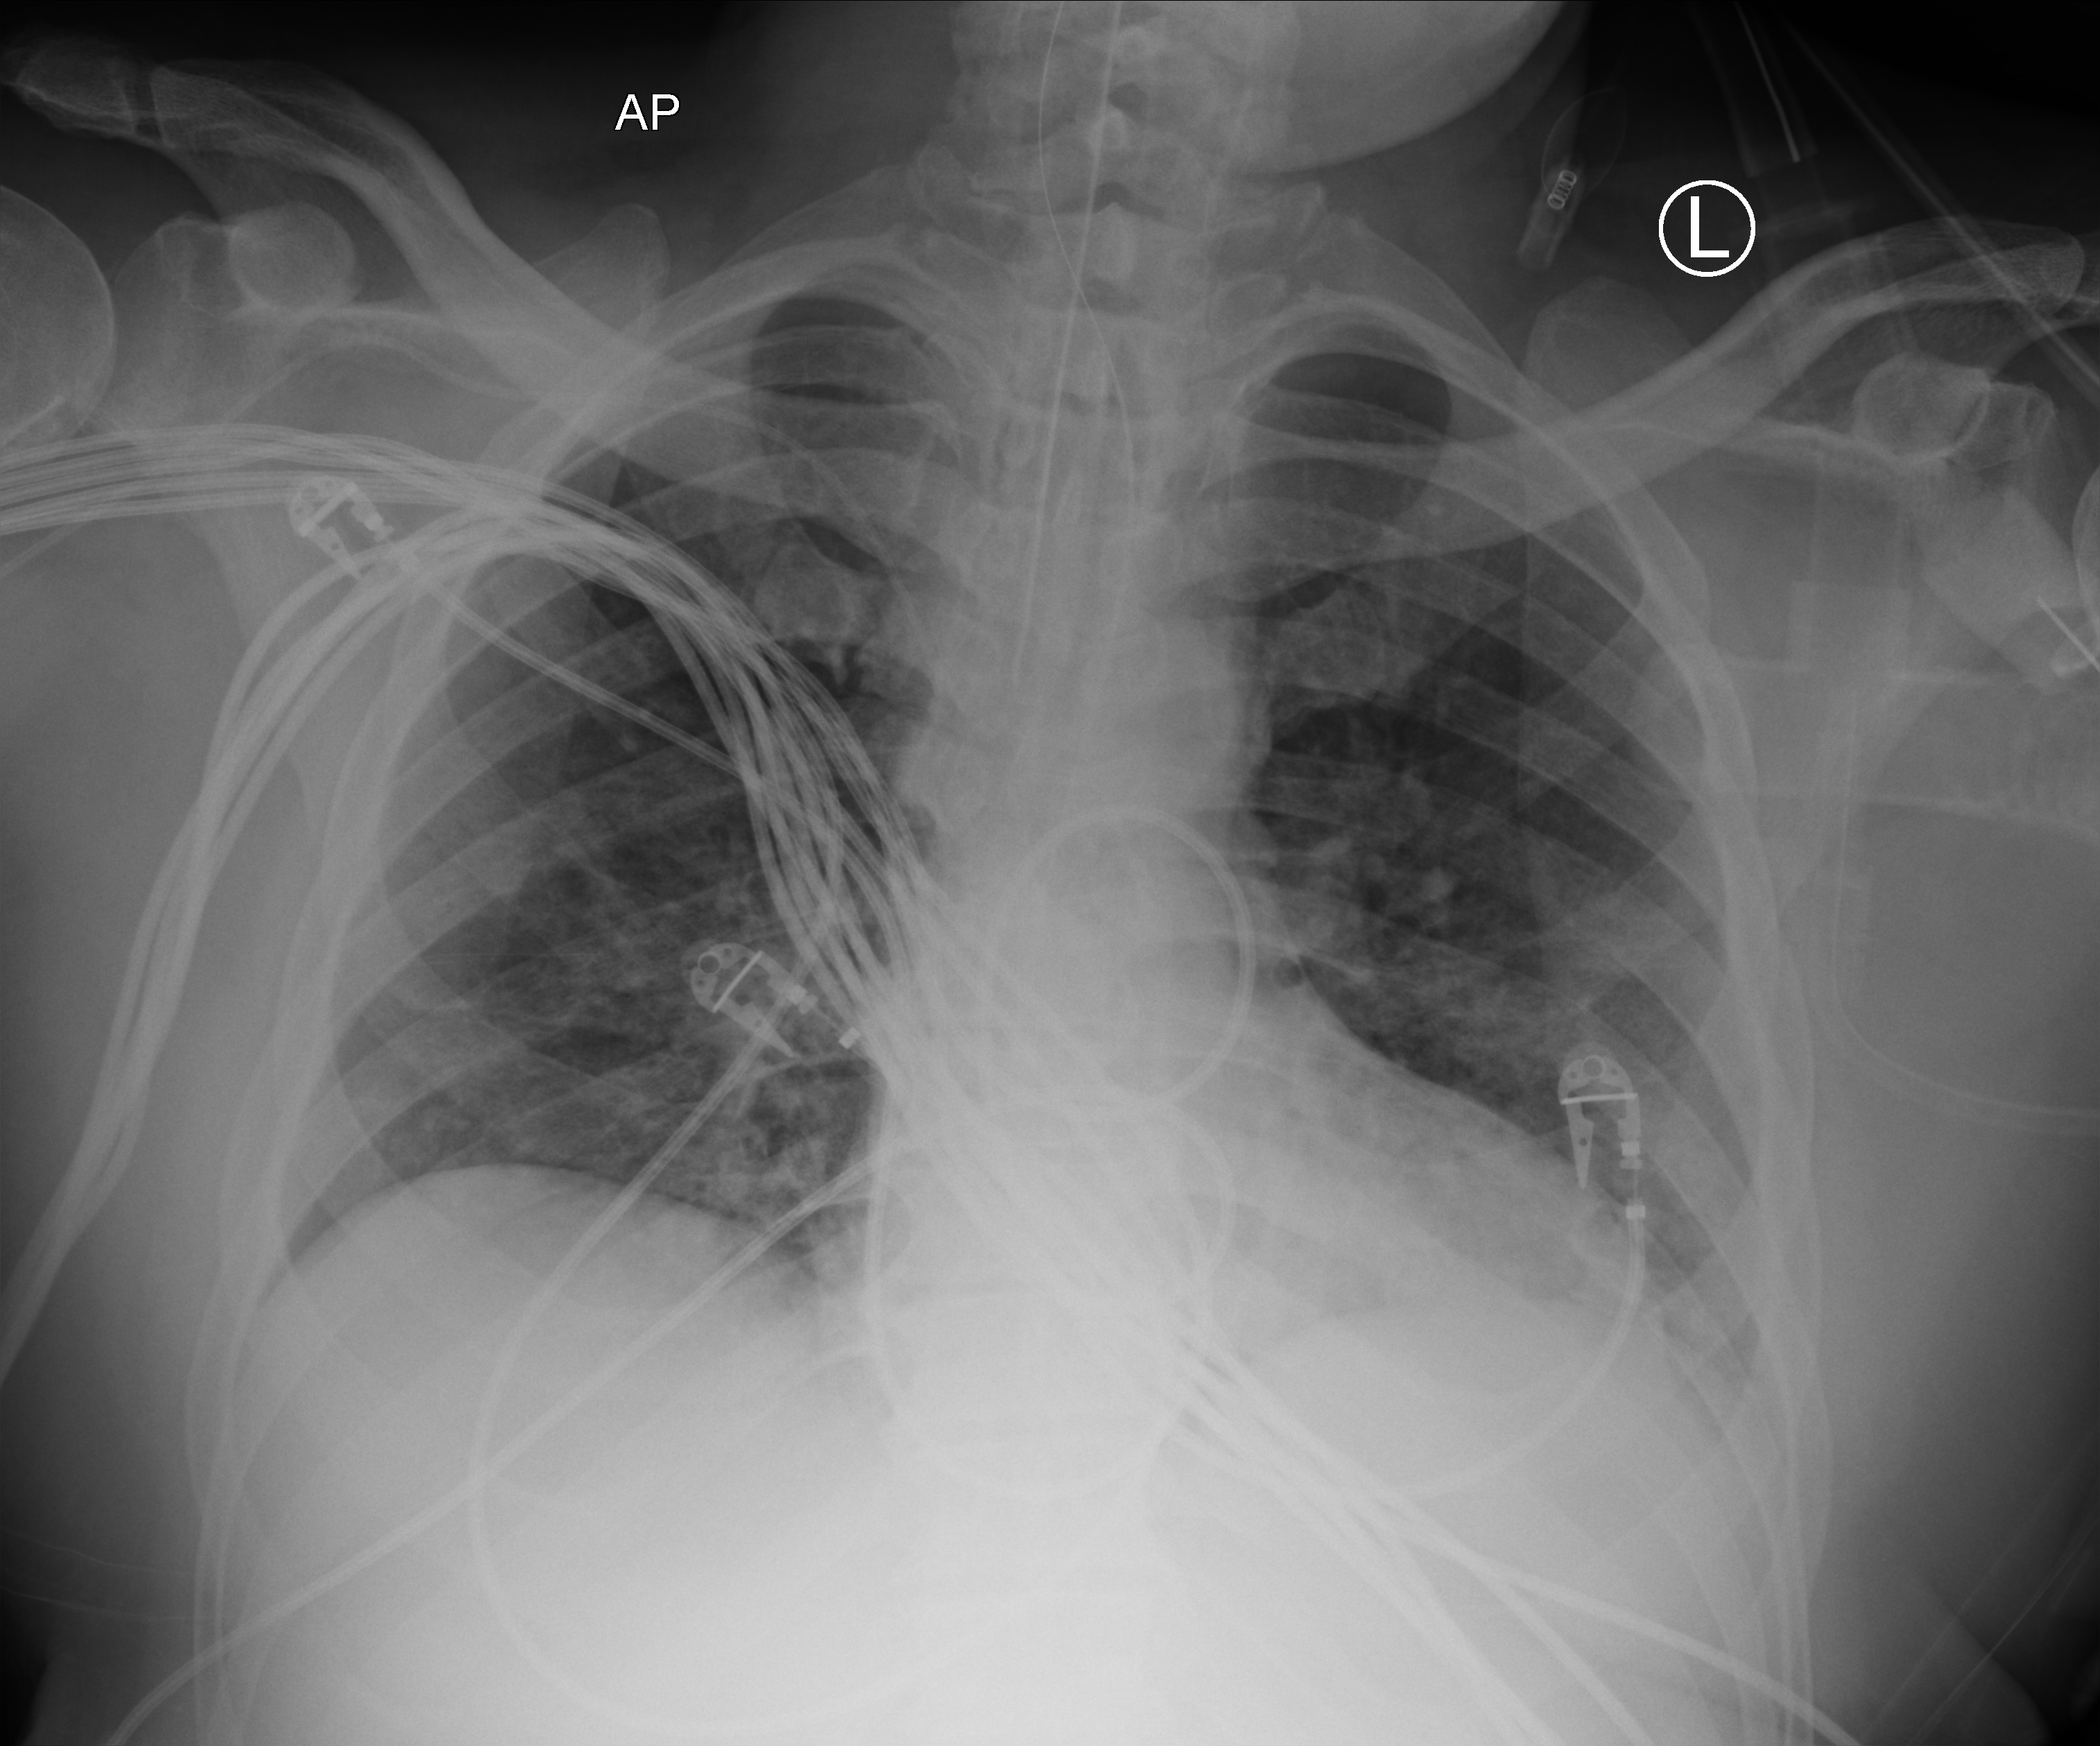
Portable chest radiograph, anteroposterior (AP) projection. Male patient hospitalised with COVID-19, age 18–59 years.
From the hospital-stay record, not from the radiograph (when in the stay this image was taken is not recorded):
- admitted to intensive care during this hospital stay: yes
- mechanically ventilated during this hospital stay: yes
- length of hospital stay: 41 days